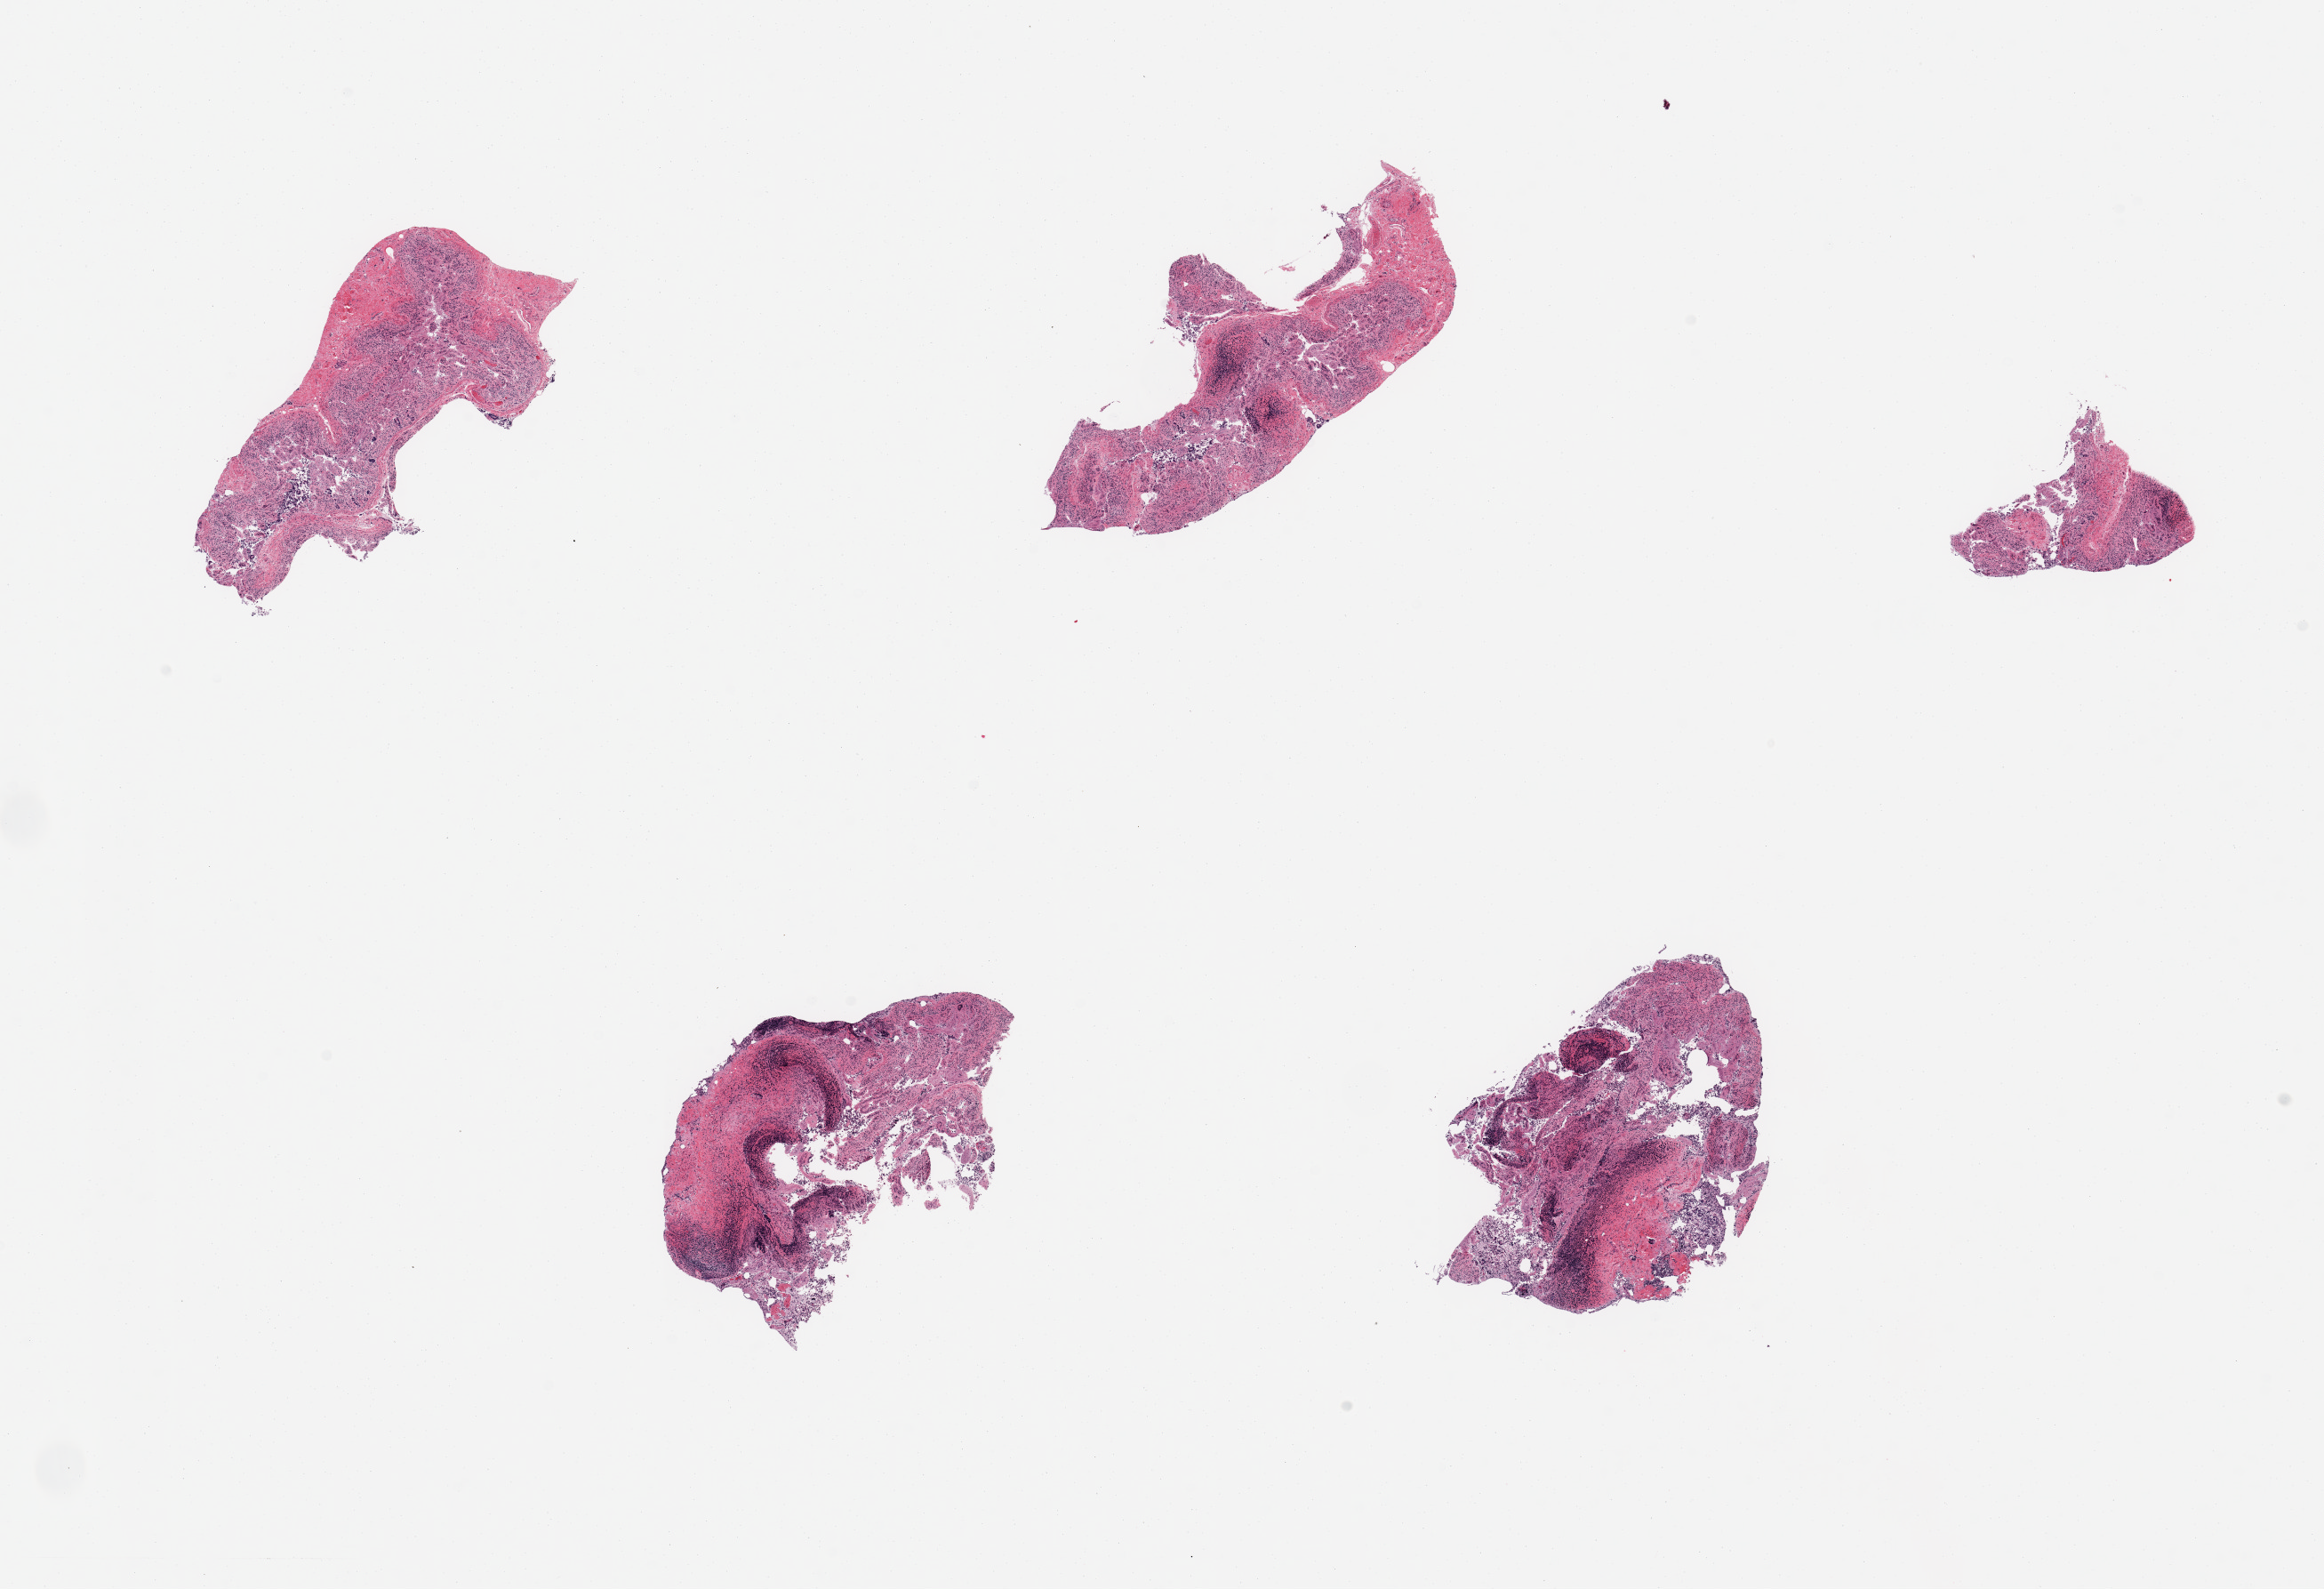
Haematoxylin and eosin whole-slide image, brightfield — shown as a low-resolution overview of the whole scanned area (about 20.7 x 14.1 mm). PAXgene-fixed, paraffin-embedded tissue. Section of ileum (target tissue). Tissue donor sample. Donor sex: male.
Review note (as recorded): 5 pieces; autolyzed mucosa and minimal lymphoid tissue.